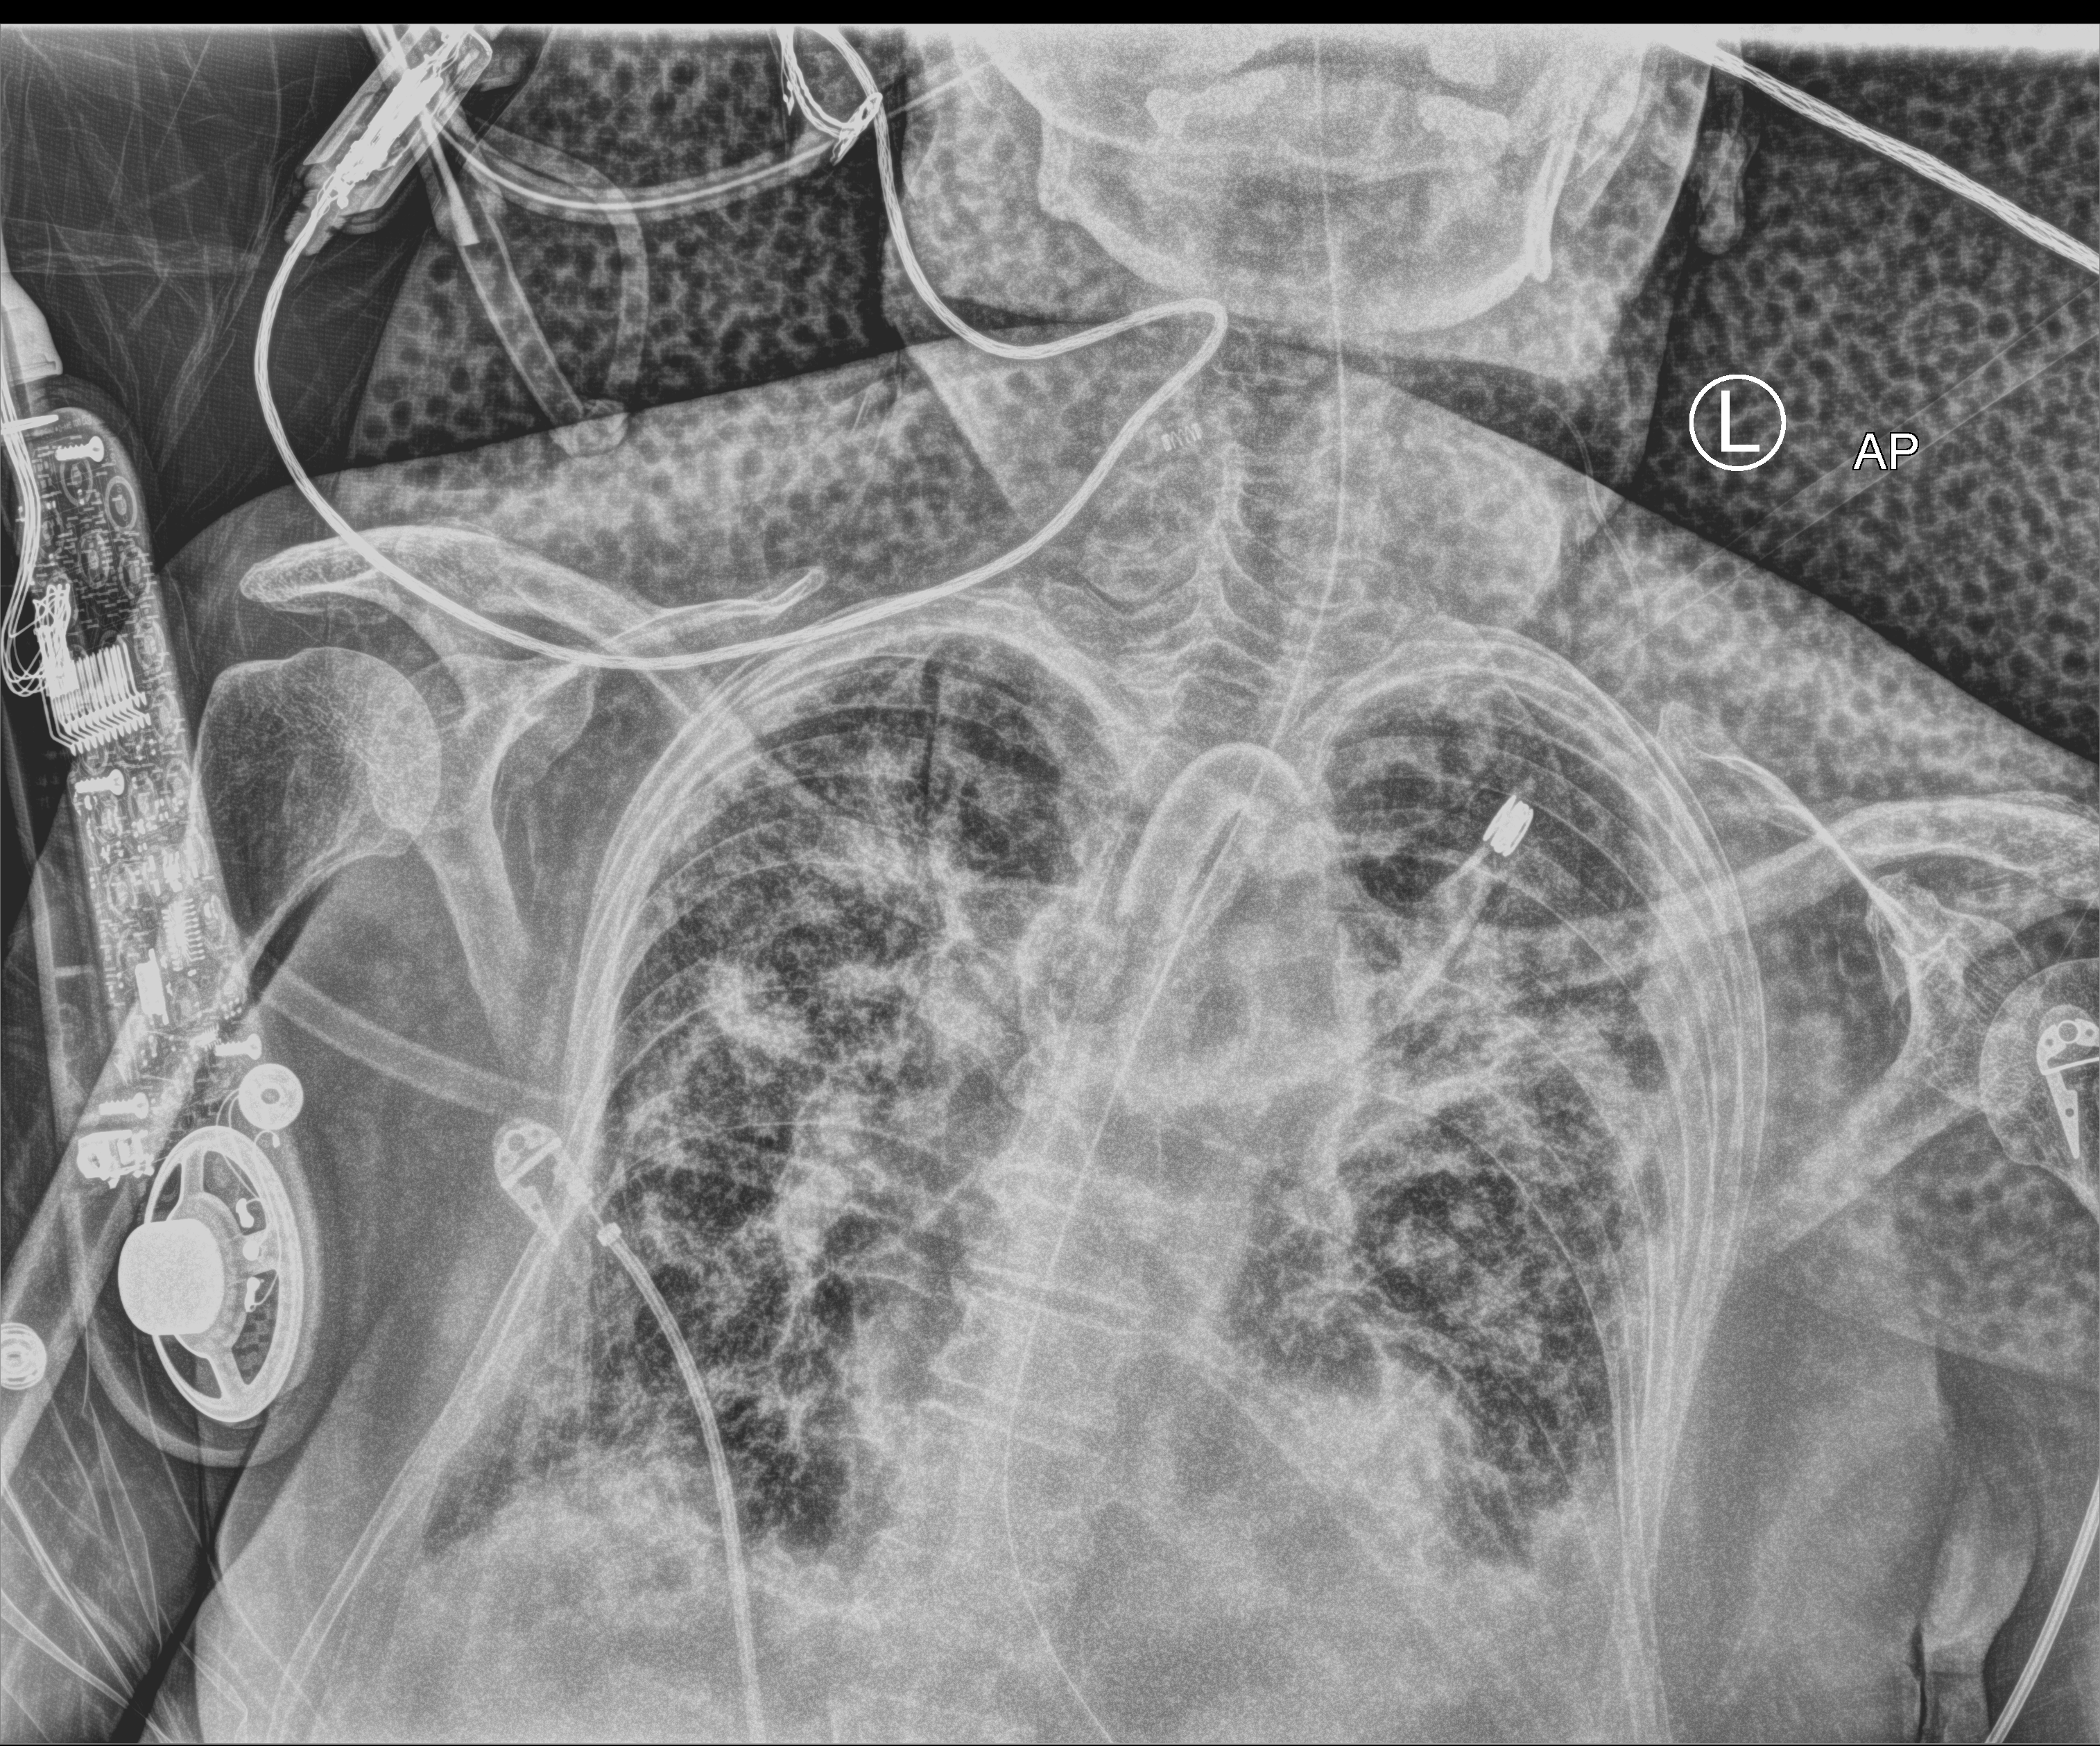
Chest X-ray (portable). Patient hospitalised with COVID-19; female, aged 75–90 years.
Admission-level facts for this patient (not findings on this image; timing relative to this image not recorded):
- mechanically ventilated during this hospital stay: yes